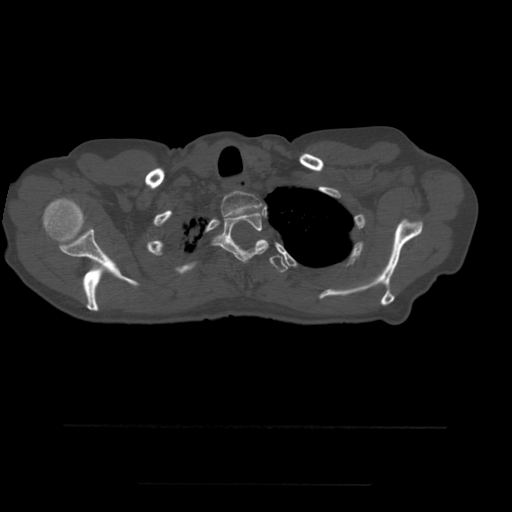
CT including the spine, one axial slice. Bone window (W 1800 / L 400 HU). 512 × 512 image matrix, field of view 350 × 350 mm. Patient age 58 years. Case-level facts recorded for this patient, not image findings: primary cancer: lung.
Annotated regions visible in this slice (semi-automatic segmentation, software-assisted and operator-edited):
- T1 vertebra: bounding box <221,191,263,217> (left, top, right, bottom; pixels)
- T2 vertebra: <213,208,269,262>
- T3 vertebra: <256,240,289,274>